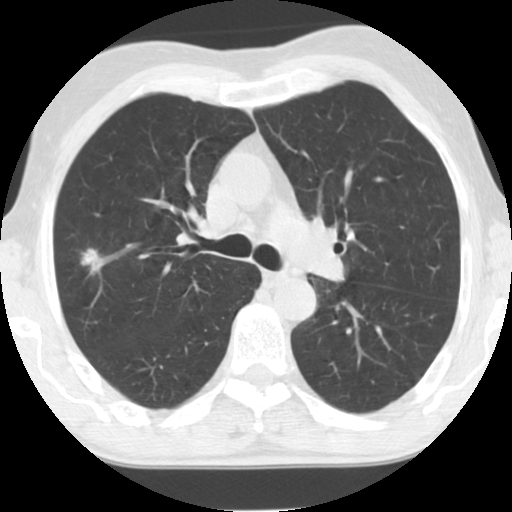
Low-dose screening chest CT, one axial slice; position 83 of 124 along the scan axis; reconstruction kernel STANDARD; 120 kVp; lung window (W 1500 / L -600 HU); 2.5 mm slice thickness; 512 × 512 image matrix, field of view 310 × 310 mm.
Outlined on this slice (expert manual segmentation):
- lesion 1 (tumor, upper lobe of right lung): bounding box <81,248,102,271> (left, top, right, bottom; pixels)